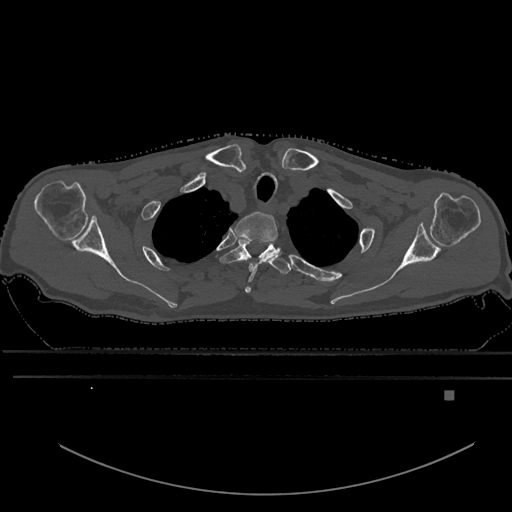
CT including the spine, one axial slice. Position 511 of 969 along the scan axis. Bone window (W 1800 / L 400 HU). 0.5 mm slice thickness. 512 × 512 image matrix, field of view 456 × 456 mm. Patient: male, 82 years. Case-level facts recorded for this patient, not image findings: primary cancer: prostate; vertebrae with lytic lesions (as recorded): T11, T9, T8, T2.
Outlined on this slice (semi-automatic segmentation, software-assisted and operator-edited):
- T1 vertebra: box from (x=234, y=212) to (x=278, y=293) px
- T2 vertebra: (x=220, y=239)–(x=290, y=274)